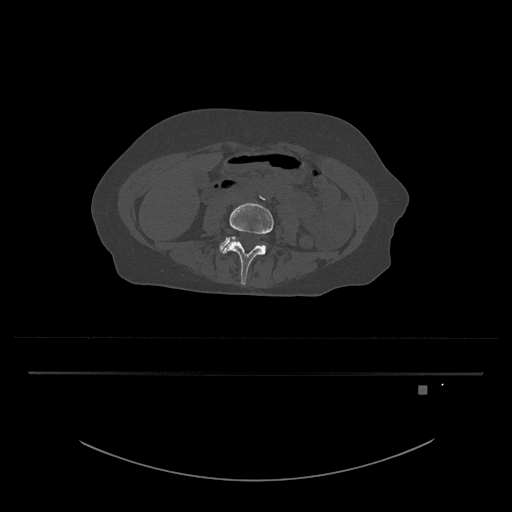
CT including the spine, one axial slice. Slice 355 of 797 in the series (ordered by position). 120 kVp. Bone window (W 1800 / L 400 HU). 0.5 mm slice thickness. 512 × 512 image matrix, field of view 500 × 500 mm. Female patient, age 57 years. From the clinical record (not read from this slice): primary cancer: cervical.
Outlined on this slice (semi-automatic segmentation, software-assisted and operator-edited):
- L4 vertebra: bounding box [x1, y1, x2, y2] px = [221, 202, 274, 285]